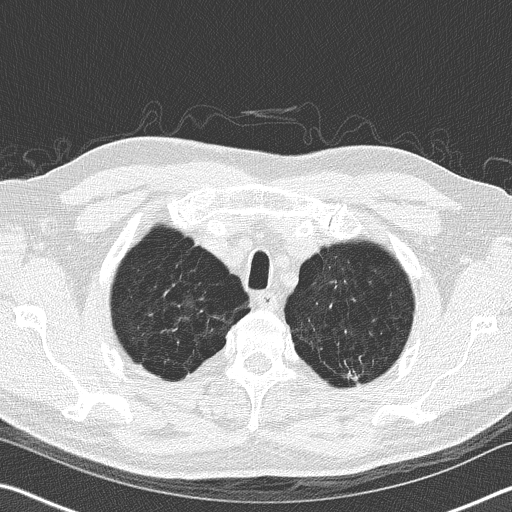
Low-dose screening chest CT, axial slice. Baseline screening round. Lung window (W 1500 / L -600 HU). Lung (sharp) reconstruction kernel (B50f). 120 kVp. Slice 24 of 167 in the series. 512 × 512 image matrix. Male participant, aged 62 years at enrolment.
• Expert reader's lesion annotation, box from (x=331, y=356) to (x=372, y=391) px.
• Reader record for this screening exam (exam-level; its link to the box is not recorded): non-calcified nodule or mass ≥4 mm, left upper lobe, 10 × 10 mm.
• Lung cancer was diagnosed 561 days after this screen (after the second annual screen): adenocarcinoma, NOS, left upper lobe, moderately differentiated (G2), stage IA (AJCC 6th edition), 10 mm at pathology.